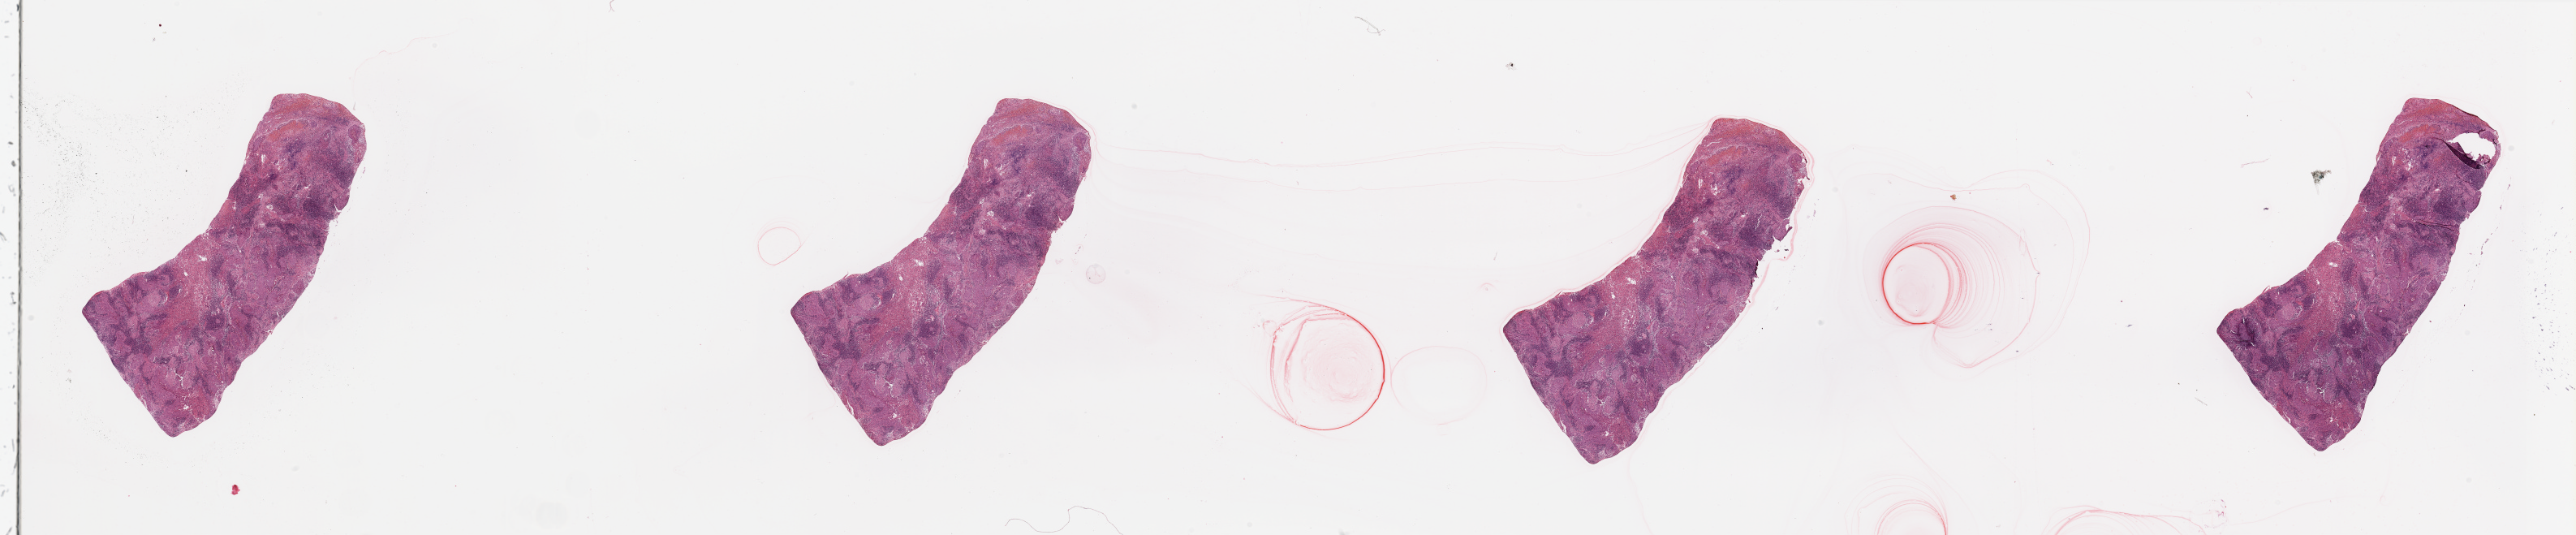
H&E-stained whole-slide image, shown as a low-resolution overview of the whole scanned area (about 50.2 x 10.4 mm). Tumour tissue sample, sampled site: larynx. Patient: male, age 68 years. Histologic grade: G3 (poorly differentiated). Pathologist review of this section (percent, as recorded): tumour nuclei 80%, necrosis 10%.
AJCC pathologic stage: I. Histologic diagnosis: Squamous cell carcinoma, NOS.